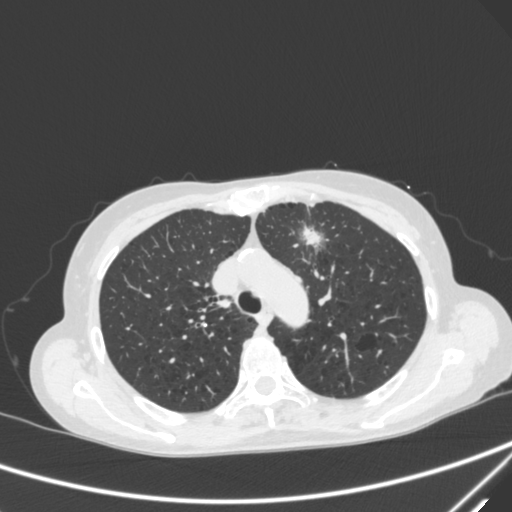
Chest CT, one axial slice; position 224 of 300 along the scan axis; 120 kVp; lung window (W 1500 / L -600 HU); 512 × 512 image matrix, field of view 350 × 350 mm. Female patient, age 71 years. Case-level facts recorded for this patient, not image findings: clinical TNM (as recorded): T1c N0 M0.
Outlined on this slice (rectangle marked by the reading radiologist):
- lung tumour (recorded histology: adenocarcinoma): bounding box [x1, y1, x2, y2] px = [292, 212, 332, 262]